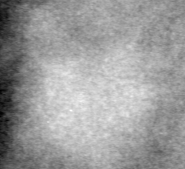
Region of interest cut from a scanned film mammogram (one marked finding); left breast; MLO view.
Finding: calcifications, morphology pleomorphic, distribution clustered; BI-RADS assessment category 4; subtlety rating 2 on a 1 (subtle) to 5 (obvious) scale; pathology result (as recorded, not read from the image): benign.